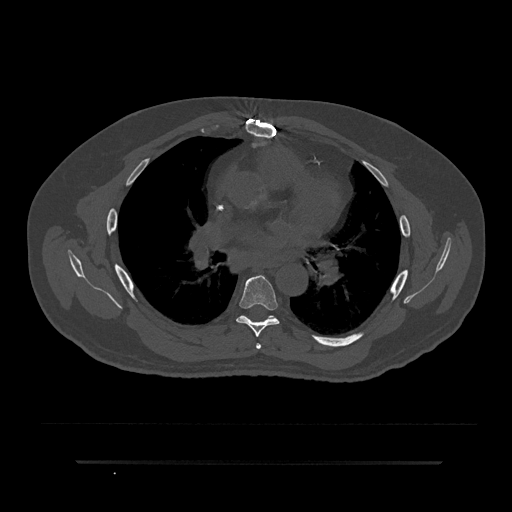
CT including the spine, one axial slice; slice 521 of 797 in the series (ordered by position); reconstruction kernel Br40s/3; bone window (W 1800 / L 400 HU); 0.5 mm slice thickness; 512 × 512 image matrix, field of view 464 × 464 mm. Male patient, age 59 years. From the clinical record (not read from this slice): primary cancer: bile ducts; vertebrae with lytic lesions (as recorded): T10.
Outlined on this slice (semi-automatic segmentation, software-assisted and operator-edited):
- T5 vertebra: bounding box [x1, y1, x2, y2] px = [256, 343, 261, 349]
- T6 vertebra: [236, 275, 280, 337]